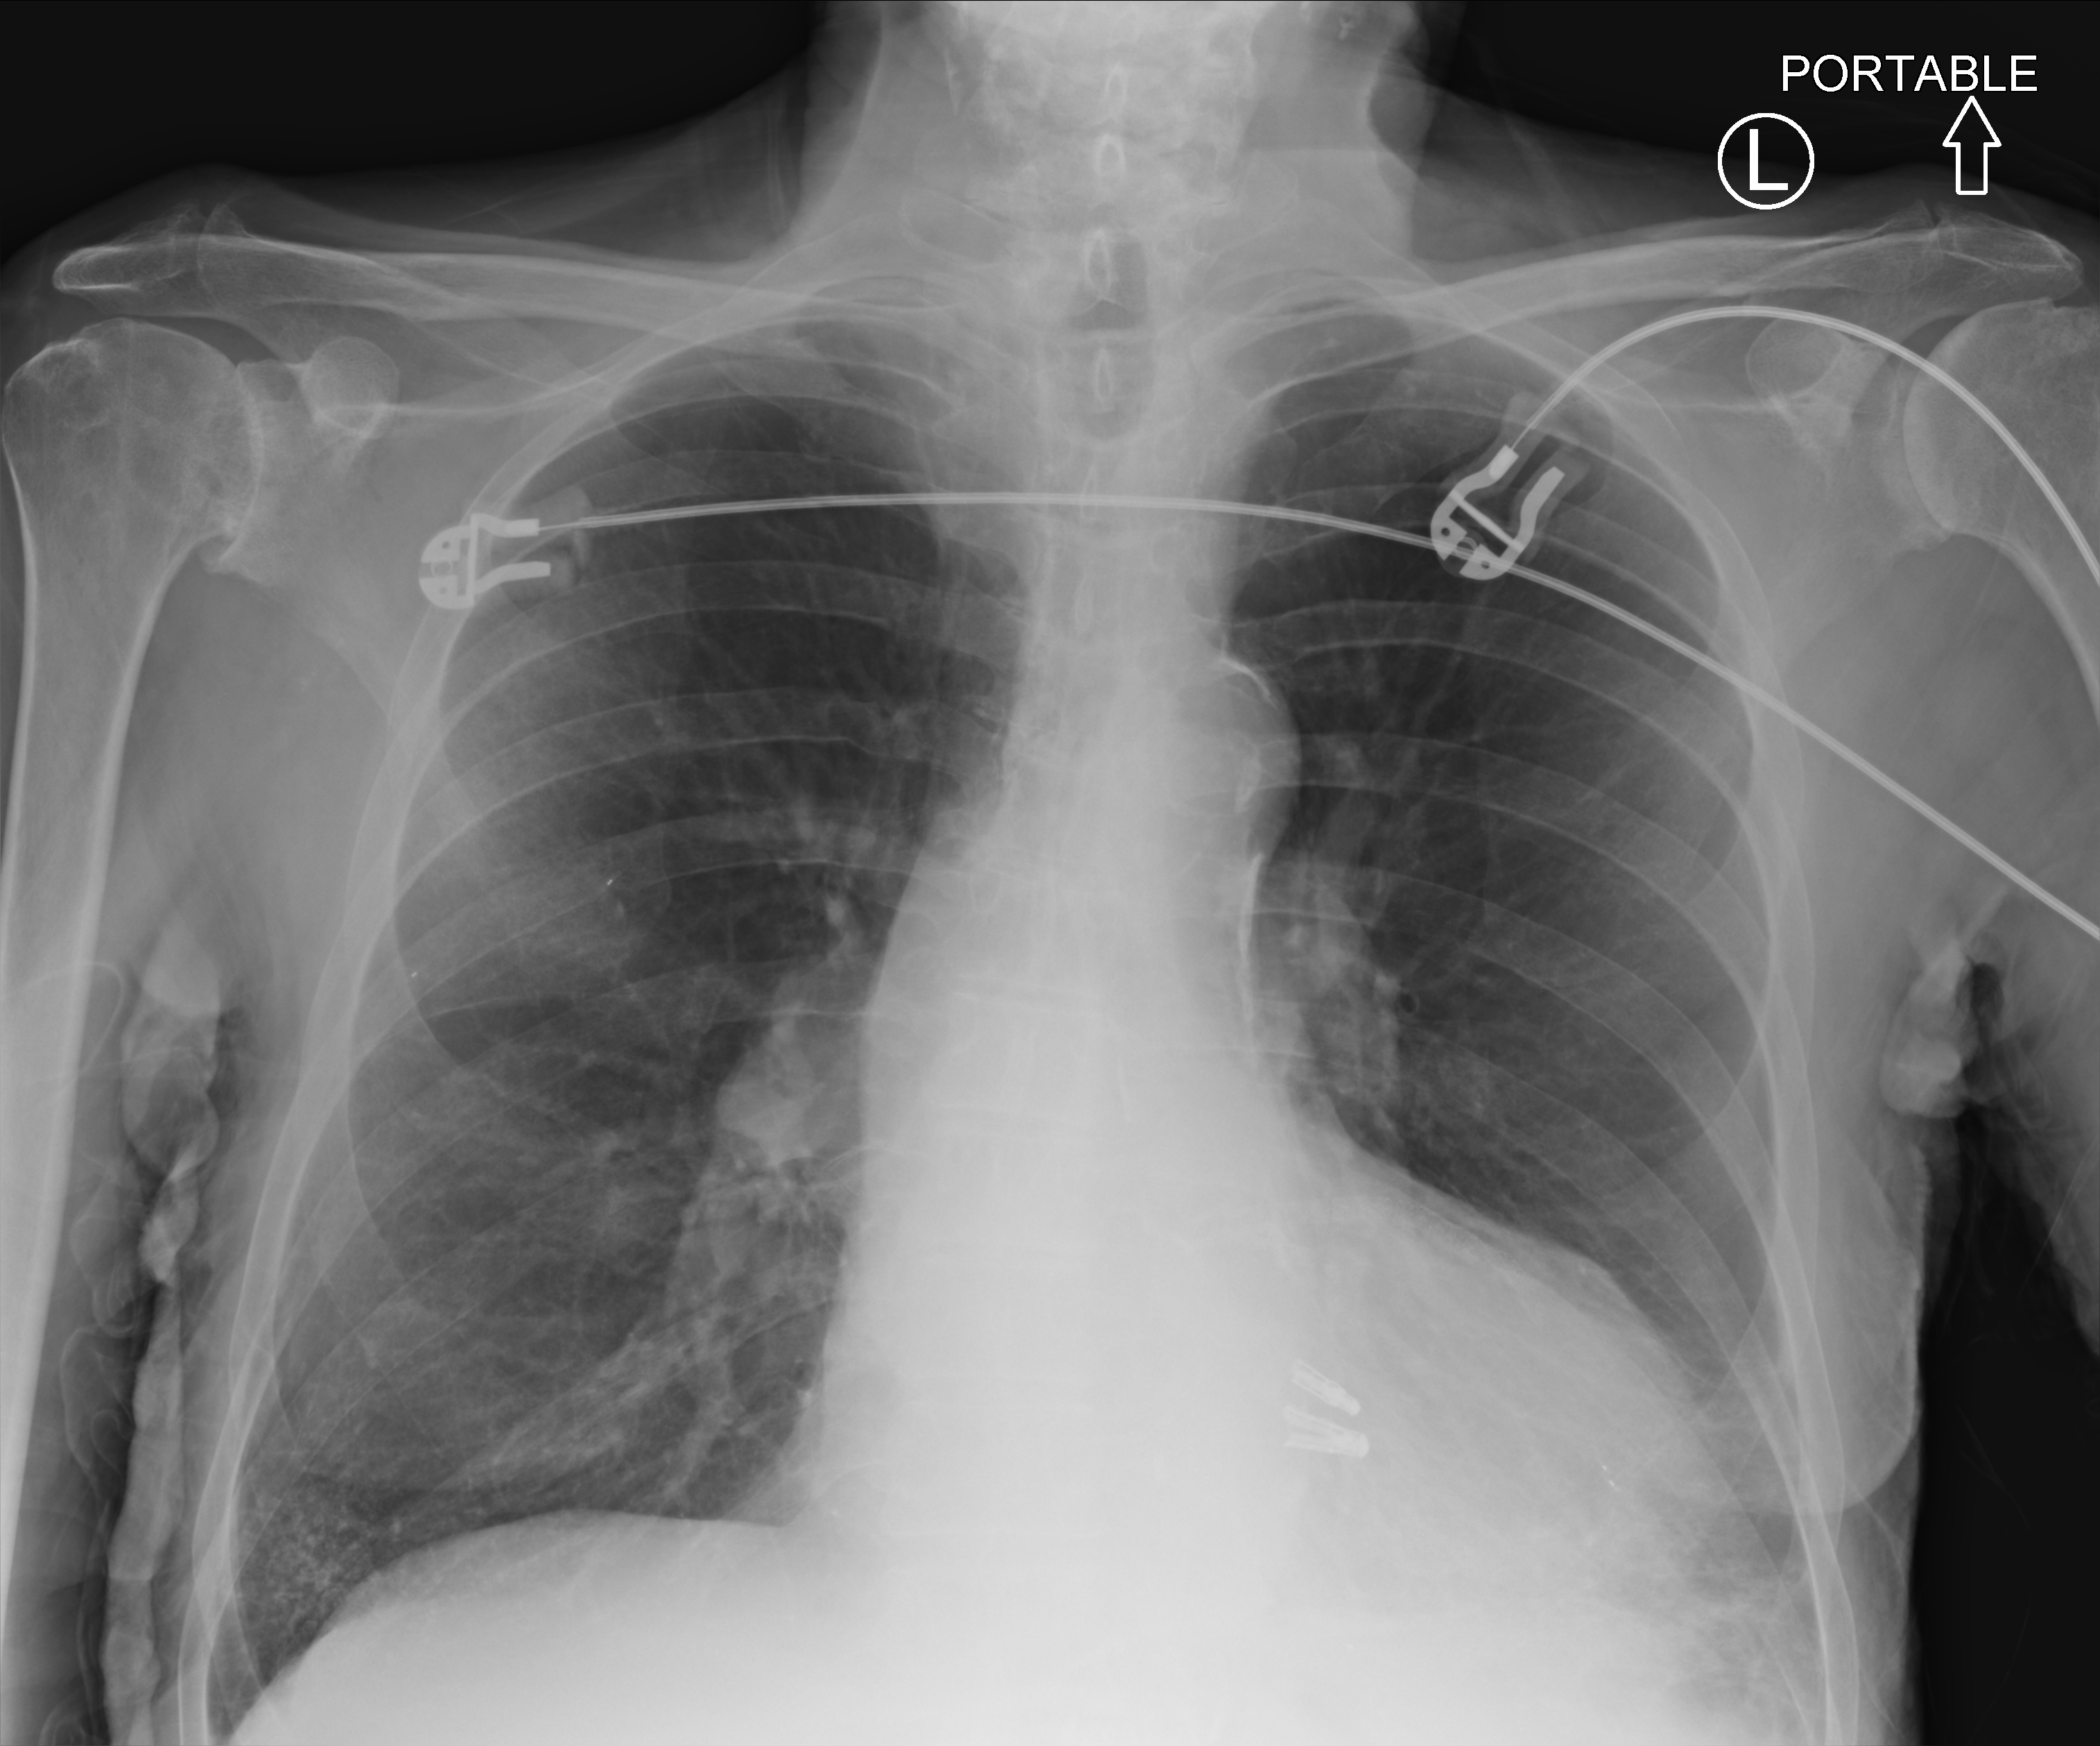
Bedside chest radiograph (computed radiography); anteroposterior (AP) projection. Patient hospitalised with COVID-19; male, aged 75–90 years.
Admission-level facts for this patient (not findings on this image; timing relative to this image not recorded):
- mechanically ventilated during this hospital stay: no
- admitted to intensive care during this hospital stay: no
- length of hospital stay: 1 day